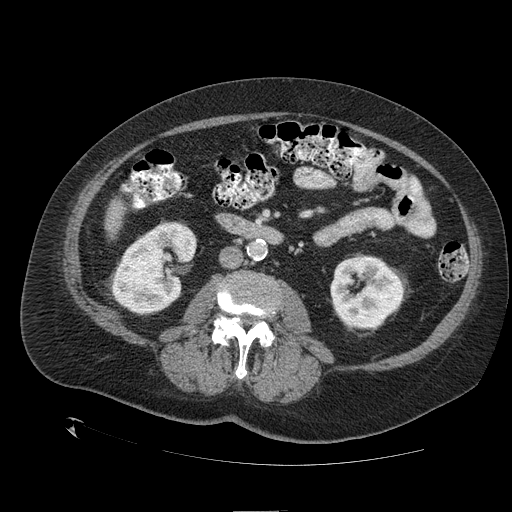
Contrast-enhanced abdominal CT (liver protocol), one axial slice; reconstruction kernel STANDARD; one of 2 acquisitions stored at this slice position; soft-tissue window (W 400 / L 40 HU); 2.5 mm slice thickness; 512 × 512 image matrix, field of view 460 × 460 mm. Case-level facts recorded for this patient, not image findings: diagnosis: hepatocellular carcinoma (patient treated with transarterial chemoembolisation; whether this scan precedes or follows treatment is not stated here); TNM stage (as recorded): Stage-I; Child-Pugh class: A; tumour differentiation: no biopsy; tumour size: 4.6 cm.
Annotated regions visible in this slice (semi-automatically segmented with operator editing):
- liver parenchyma outside the tumour (the mass and vessels are separate outlines, so this box may not span the whole liver): bounding box [x1, y1, x2, y2] px = [106, 212, 120, 235]